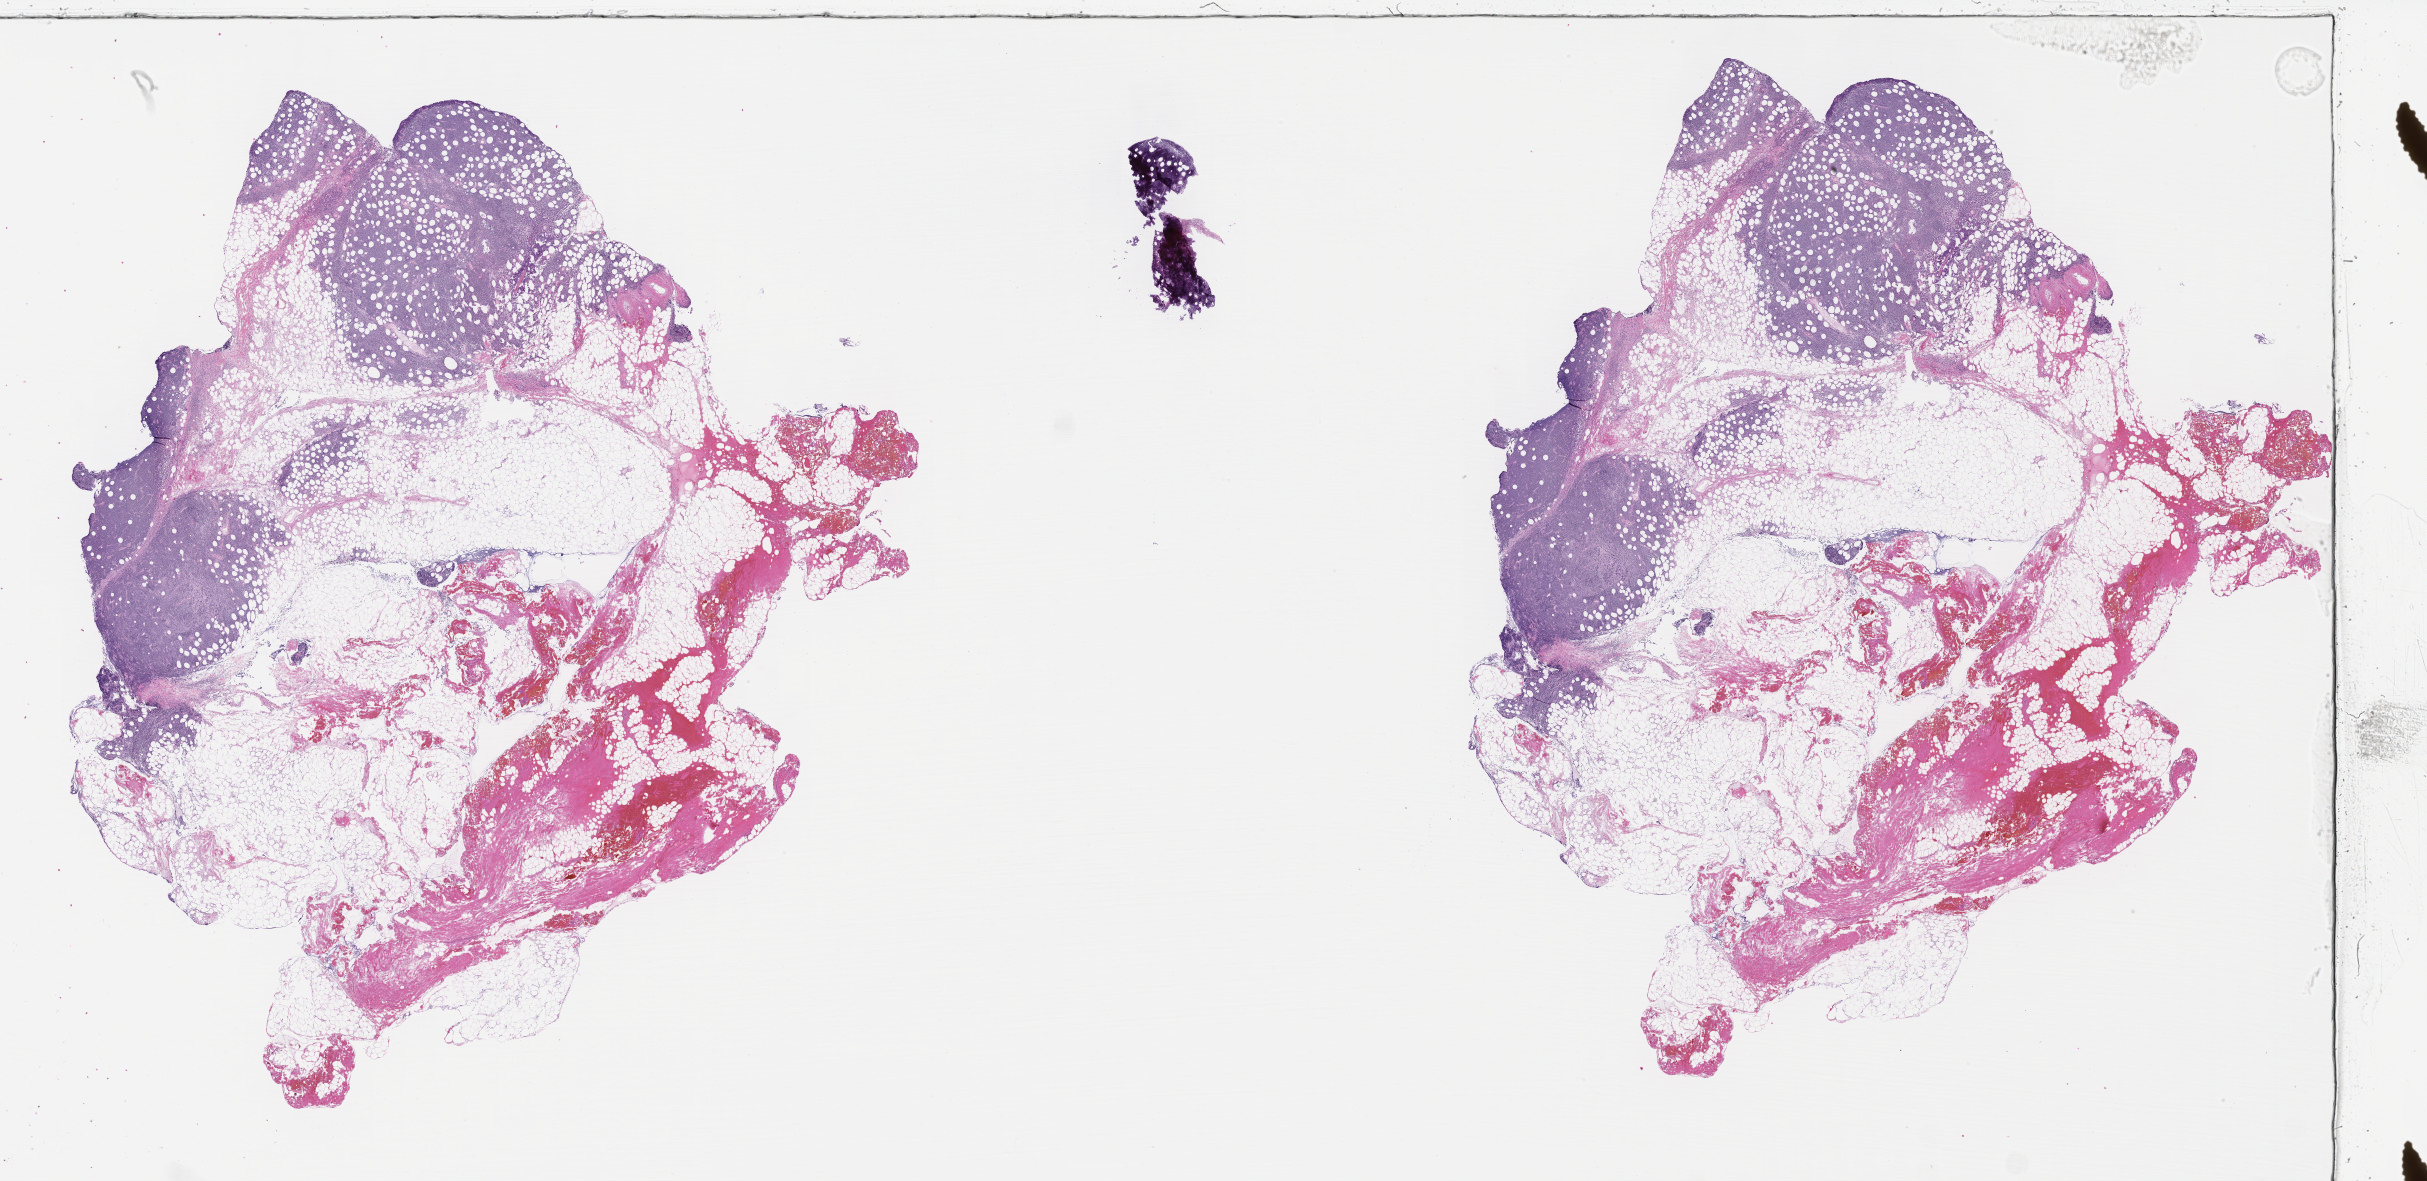
Whole-slide image, haematoxylin and eosin stain, shown as a low-resolution overview of the whole scanned area (about 39.2 x 19.1 mm), formalin-fixed paraffin-embedded section, specimen: primary tumor, site: upper limb lymph node. Patient: male, aged 76. Composition of this section per pathologist review: tumor cells 30%, tumor nuclei 75%, stromal cells 20%, necrosis 5%, normal cells 45%. Infiltration values recorded for this section: lymphocyte infiltration 20%, monocyte infiltration 30%, neutrophil infiltration 10%.
* Ann Arbor stage (patient): Stage I
* diagnosis: Burkitt lymphoma, NOS